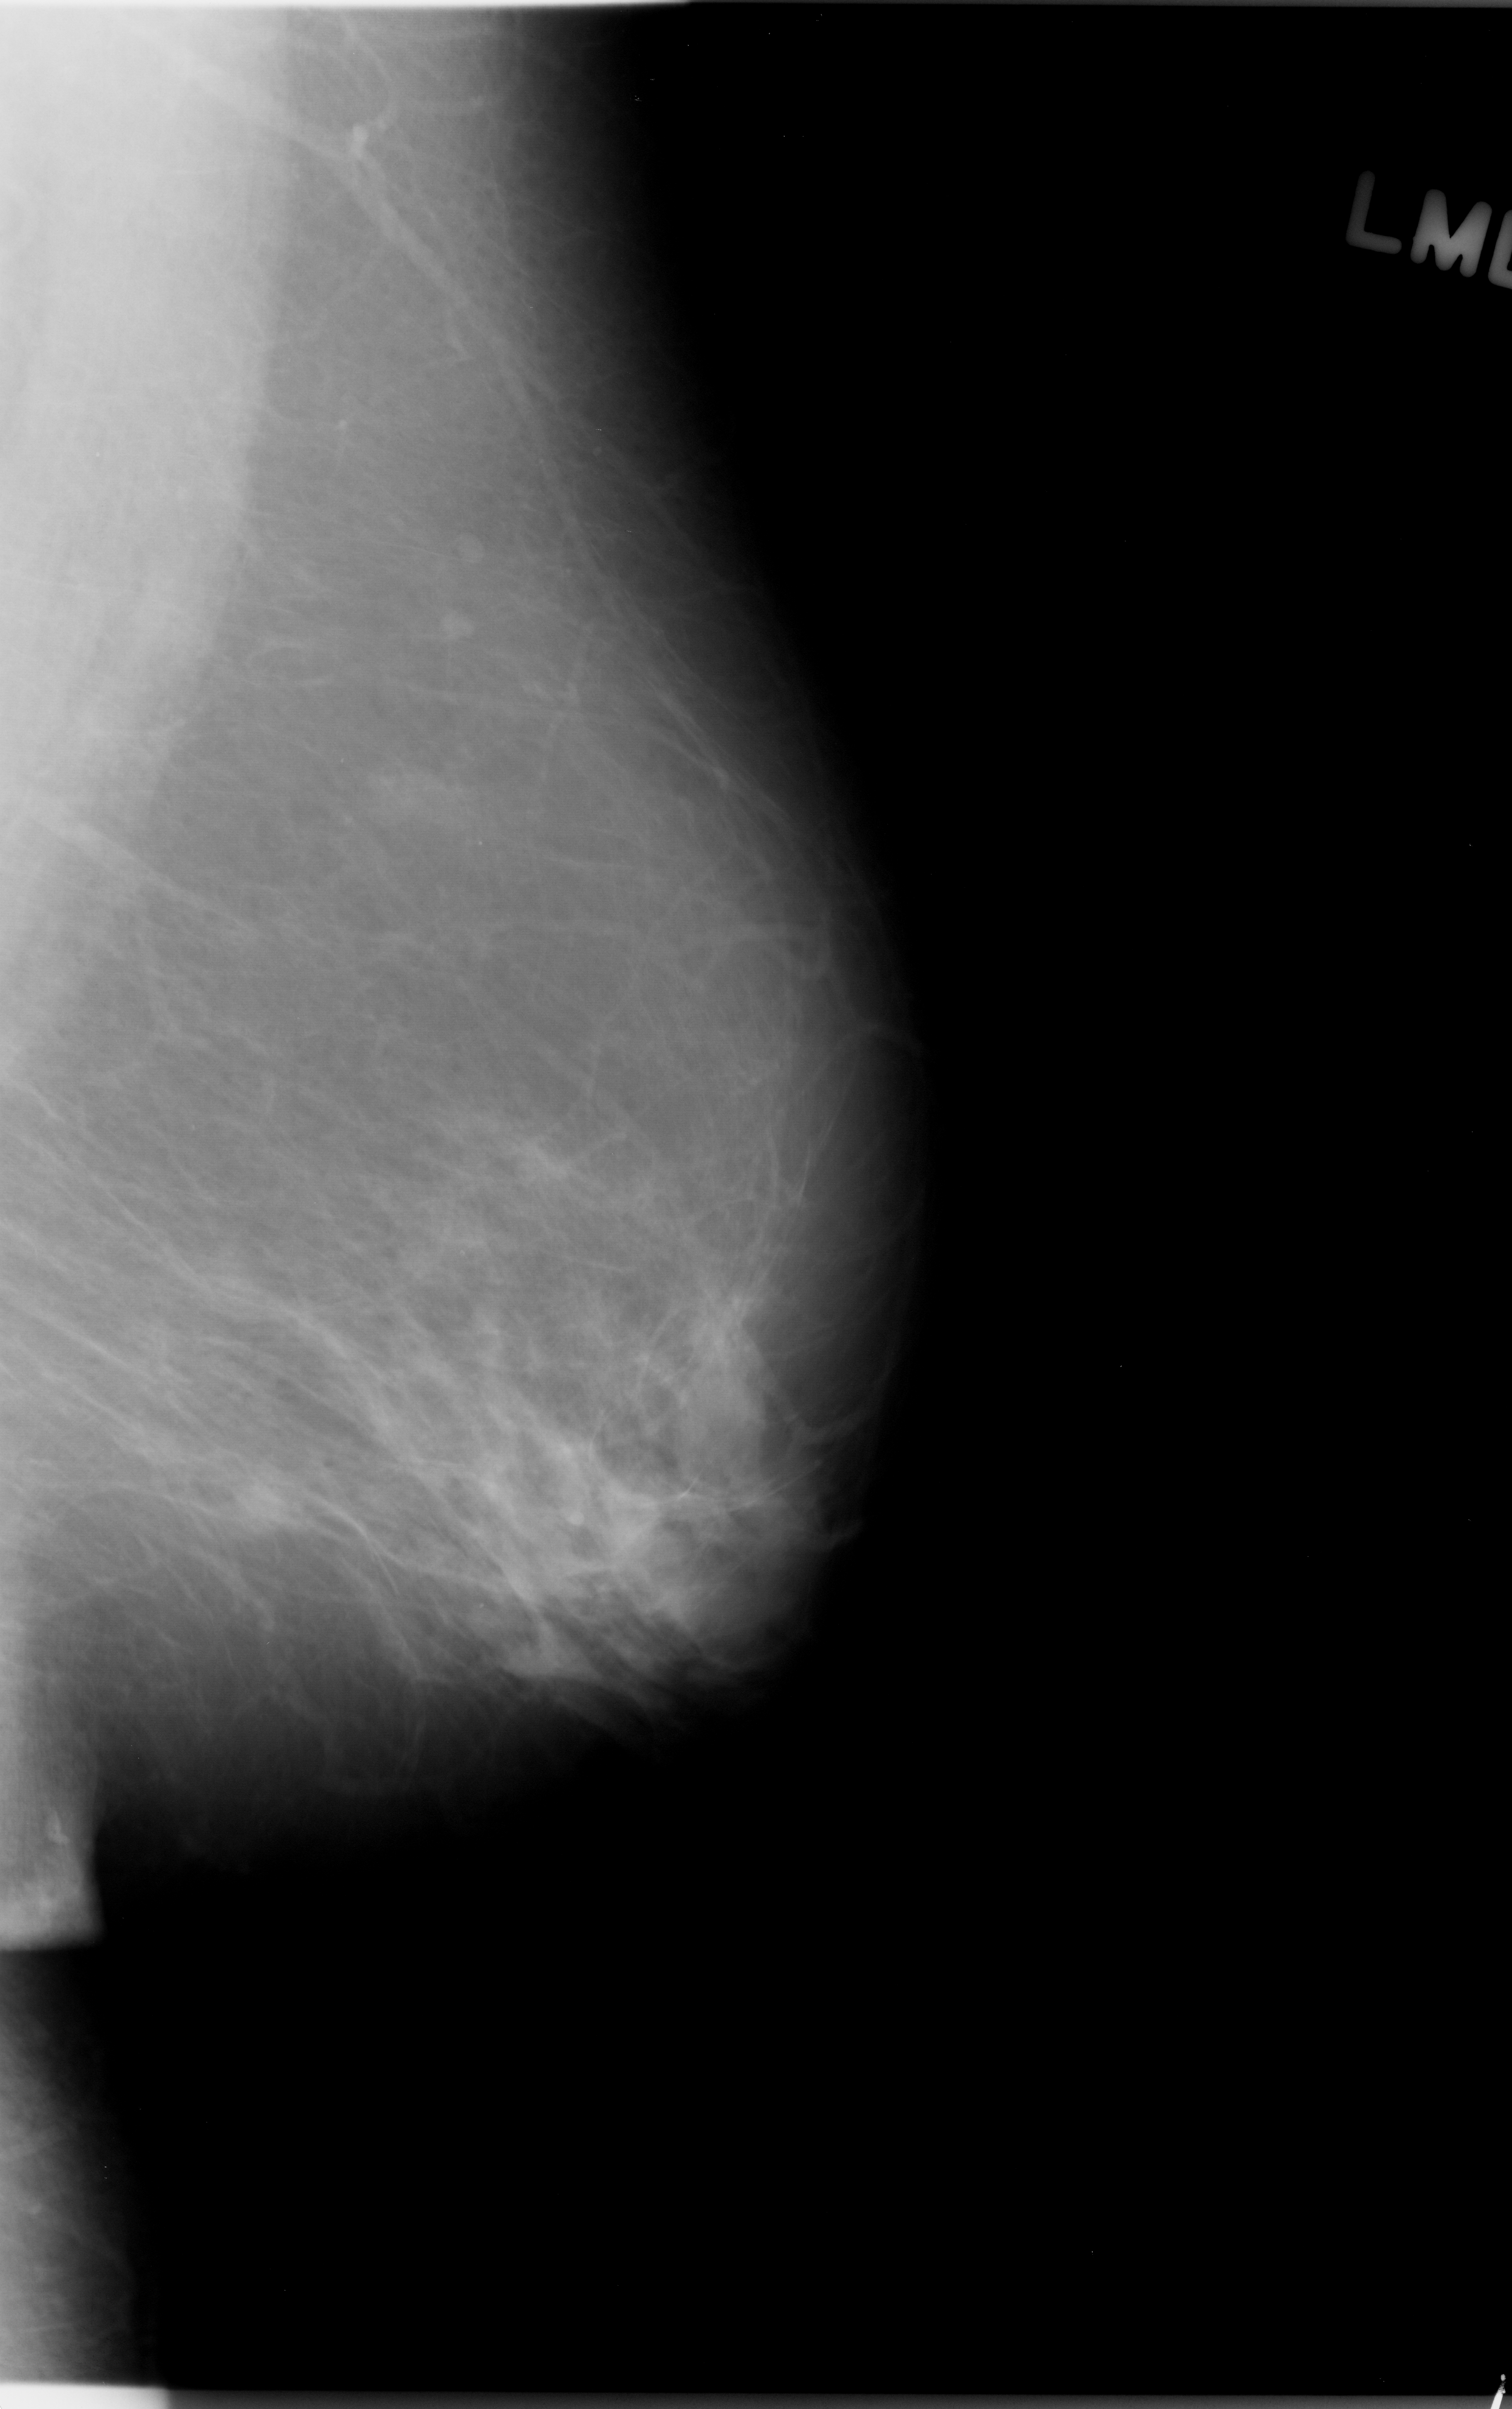
Digitized screen-film mammogram. Left breast. Mediolateral oblique (MLO) view. Breast composition: almost entirely fatty (BI-RADS density category 1 of 4). 1512 × 2409 image matrix.
Marked abnormalities (boxes around the expert regions of interest):
- mass, shape oval, margins ill defined; BI-RADS assessment category 5; subtlety rating 2 on a 1 (subtle) to 5 (obvious) scale; pathology (as recorded): malignant: box from (x=211, y=1454) to (x=321, y=1555) px